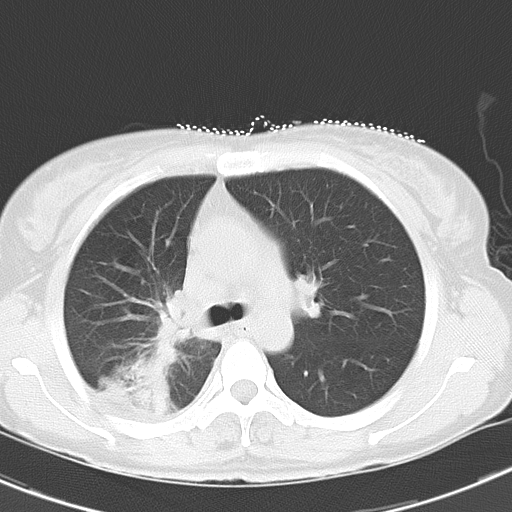
Chest CT, one axial slice; position 20 of 29 along the scan axis; reconstruction kernel B70f; lung window (W 1500 / L -600 HU); 8 mm slice thickness; 512 × 512 image matrix, field of view 300 × 300 mm. Female patient, age 47 years. From the clinical record (not read from this slice): clinical TNM (as recorded): T1c N3 M0.
Outlined on this slice (rectangle marked by the reading radiologist):
- lung tumour (recorded histology: adenocarcinoma): box from (x=94, y=327) to (x=180, y=426) px